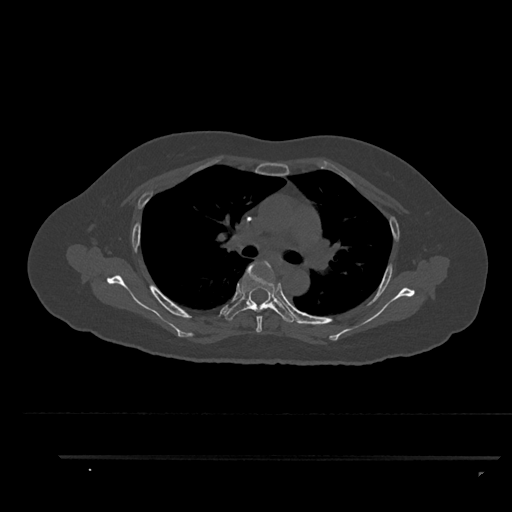
CT including the spine, one axial slice; position 615 of 797 along the scan axis; reconstruction kernel Br40s/3; 120 kVp; bone window (W 1800 / L 400 HU); 0.5 mm slice thickness; 512 × 512 image matrix, field of view 408 × 408 mm. Female patient, age 44 years. Case-level facts recorded for this patient, not image findings: primary cancer: renal; vertebrae with lytic lesions (as recorded): L1.
Annotated regions visible in this slice (semi-automatically segmented with operator editing):
- T4 vertebra: bounding box [x1, y1, x2, y2] px = [256, 260, 273, 333]
- T5 vertebra: [222, 261, 296, 323]